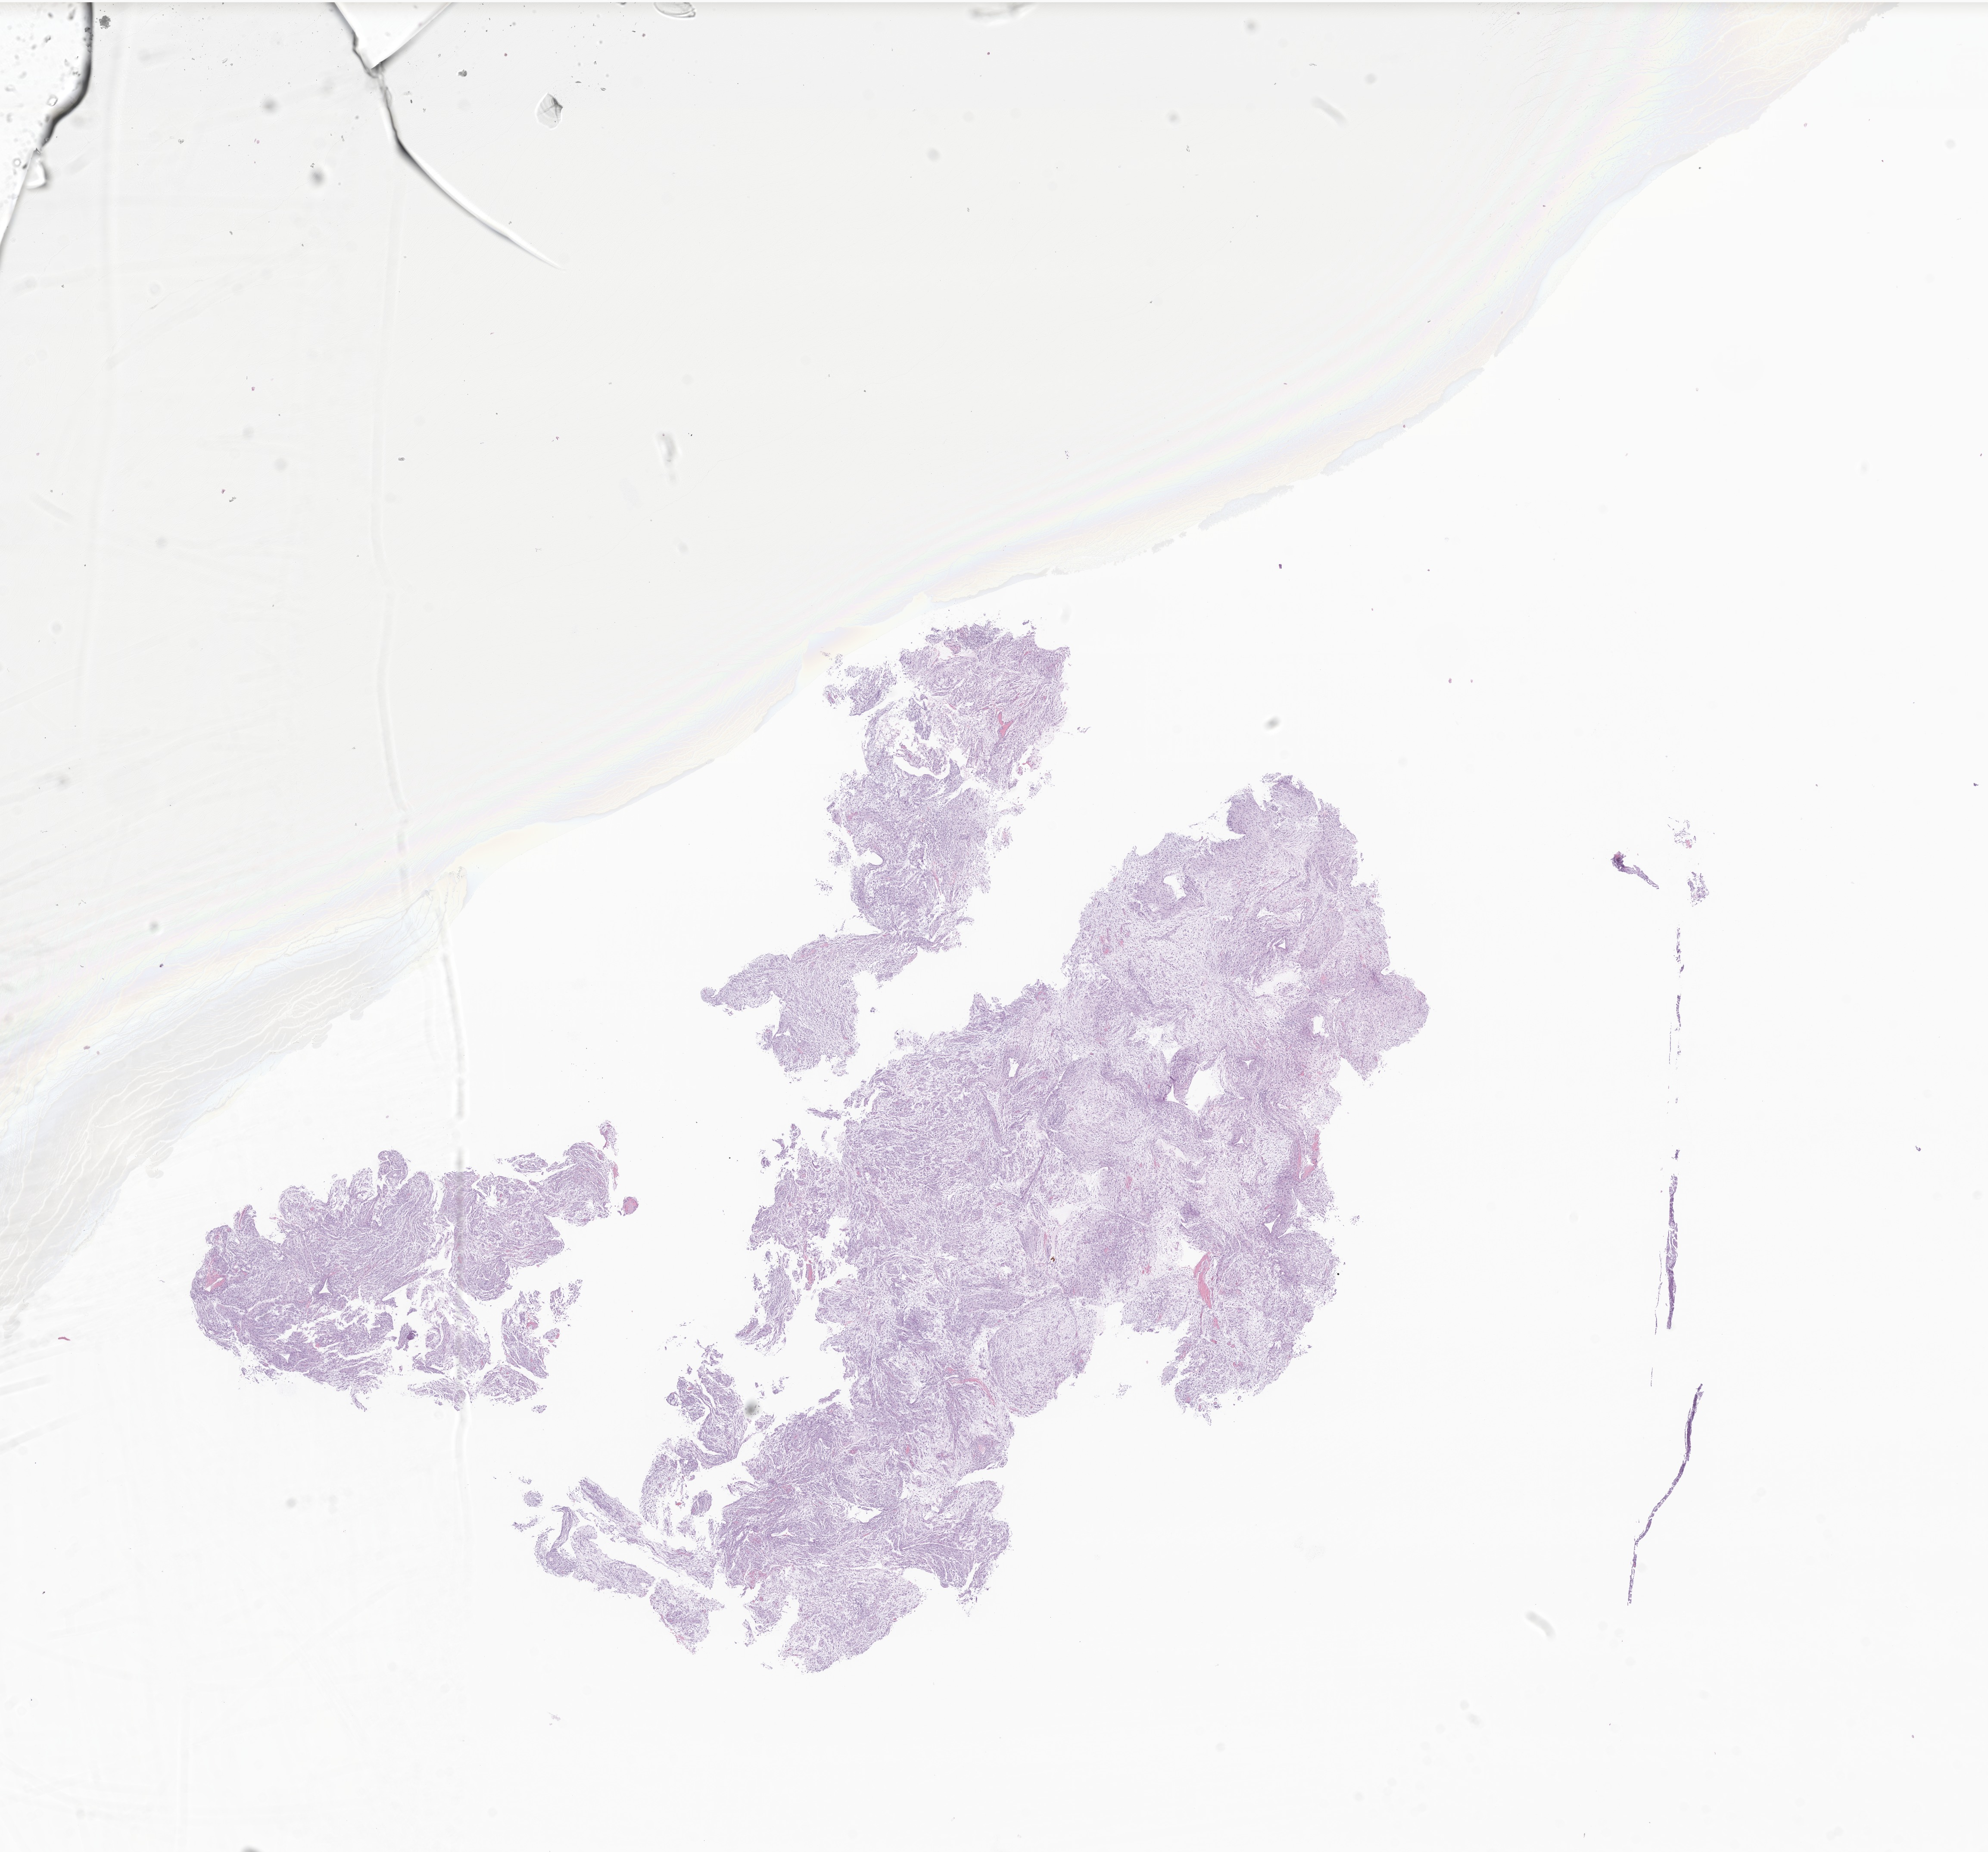
Whole-slide image, hematoxylin and eosin (H&E) stain of tumor tissue from the brain — whole scanned area (about 19.5 x 18.1 mm) shown as a low-resolution overview; formalin-fixed paraffin-embedded section. Patient: female, age 189 months (15 years 9 months).
• diagnosis (ICD-O-3 morphology term): Neoplasm, uncertain whether benign or malignant